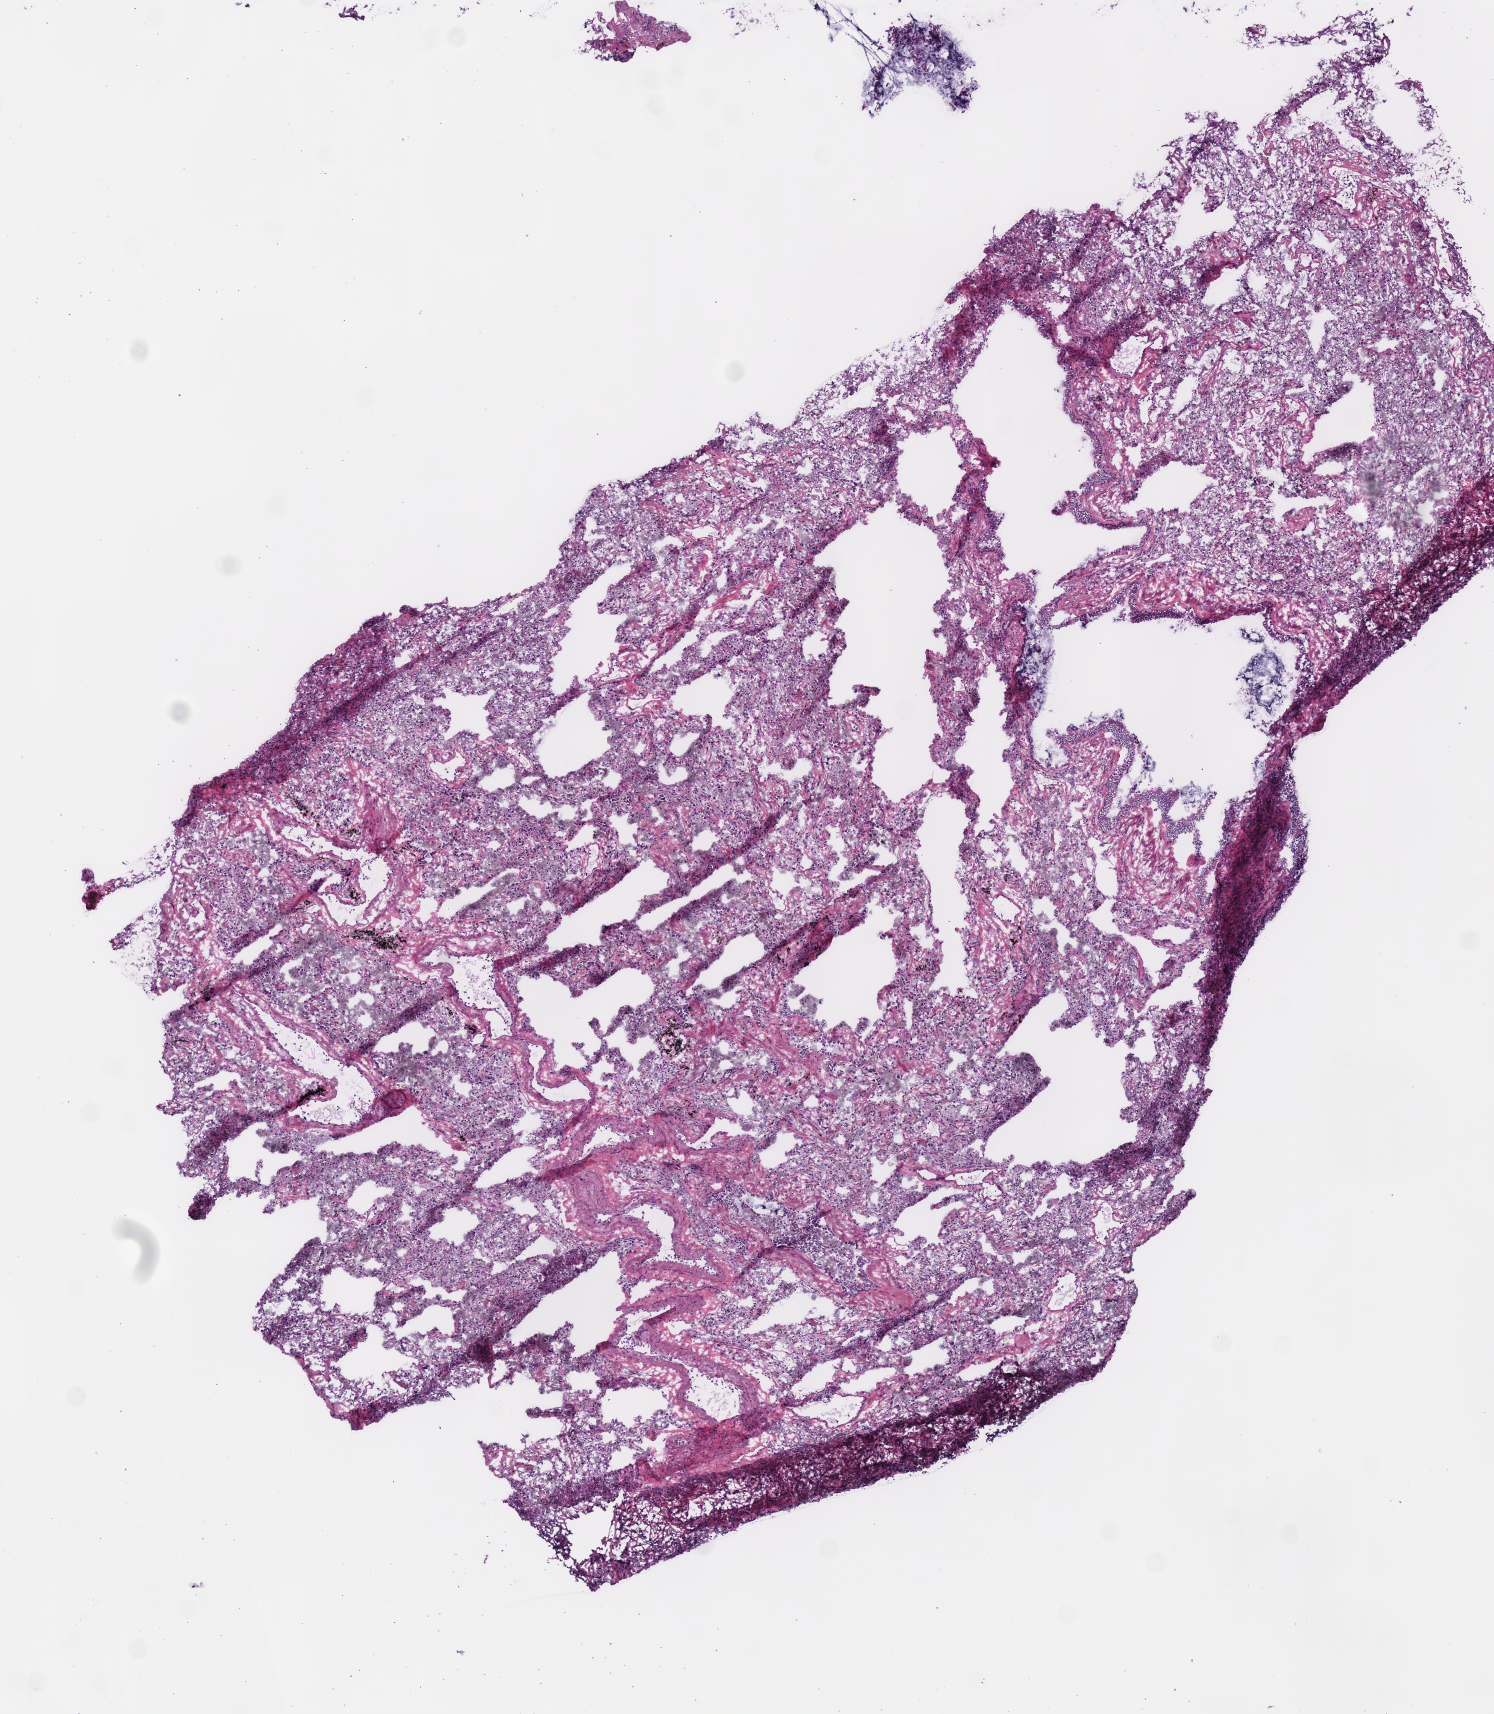
Hematoxylin and eosin (H&E) stained whole-slide image — a low-resolution overview of the entire scanned area, about 5.9 x 6.7 mm (acquisition: 40x scan); frozen section from the top of the tissue portion; sample: solid tissue normal (non-tumour tissue), lung. Patient: female, age at initial diagnosis 61 years.
This section: solid tissue normal sample (biorepository sample class). Patient diagnosis: Adenocarcinoma, NOS (upper lobe, lung).